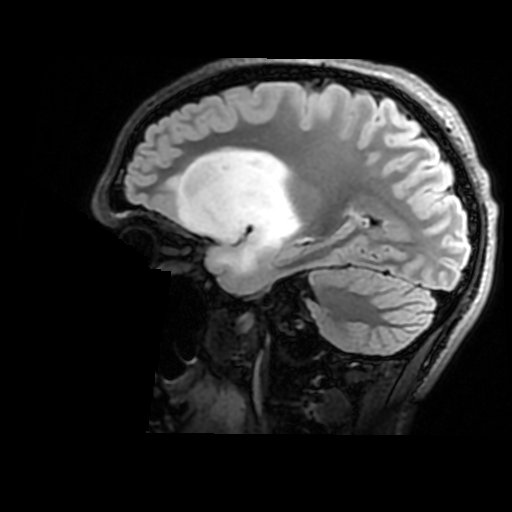
Brain MRI from a brain-tumour surgery series, one sagittal slice; position 113 of 176 along the scan axis; T2 FLAIR; 1 mm slice thickness; 512 × 512 image matrix. Case-level facts recorded for this patient, not image findings: histopathology: Astrocytoma; WHO grade: 2; IDH mutation: yes; tumour location: Right Insular.
Annotated regions visible in this slice (outlined manually by an expert reader):
- tumour: box from (x=179, y=148) to (x=298, y=278) px